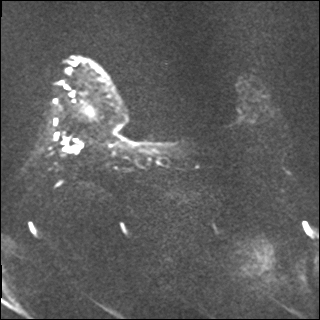
Breast MRI, one axial slice. Slice 8 of 37 in the series (ordered by position). Diffusion-weighted series; image 2 of 4 stored at this slice position (different b-values; order by instance number). 1.5 T. 320 × 320 image matrix. Female patient.
Annotated regions visible in this slice (outlined manually by an expert reader):
- tumour on diffusion-weighted imaging: box from (x=61, y=135) to (x=84, y=154) px